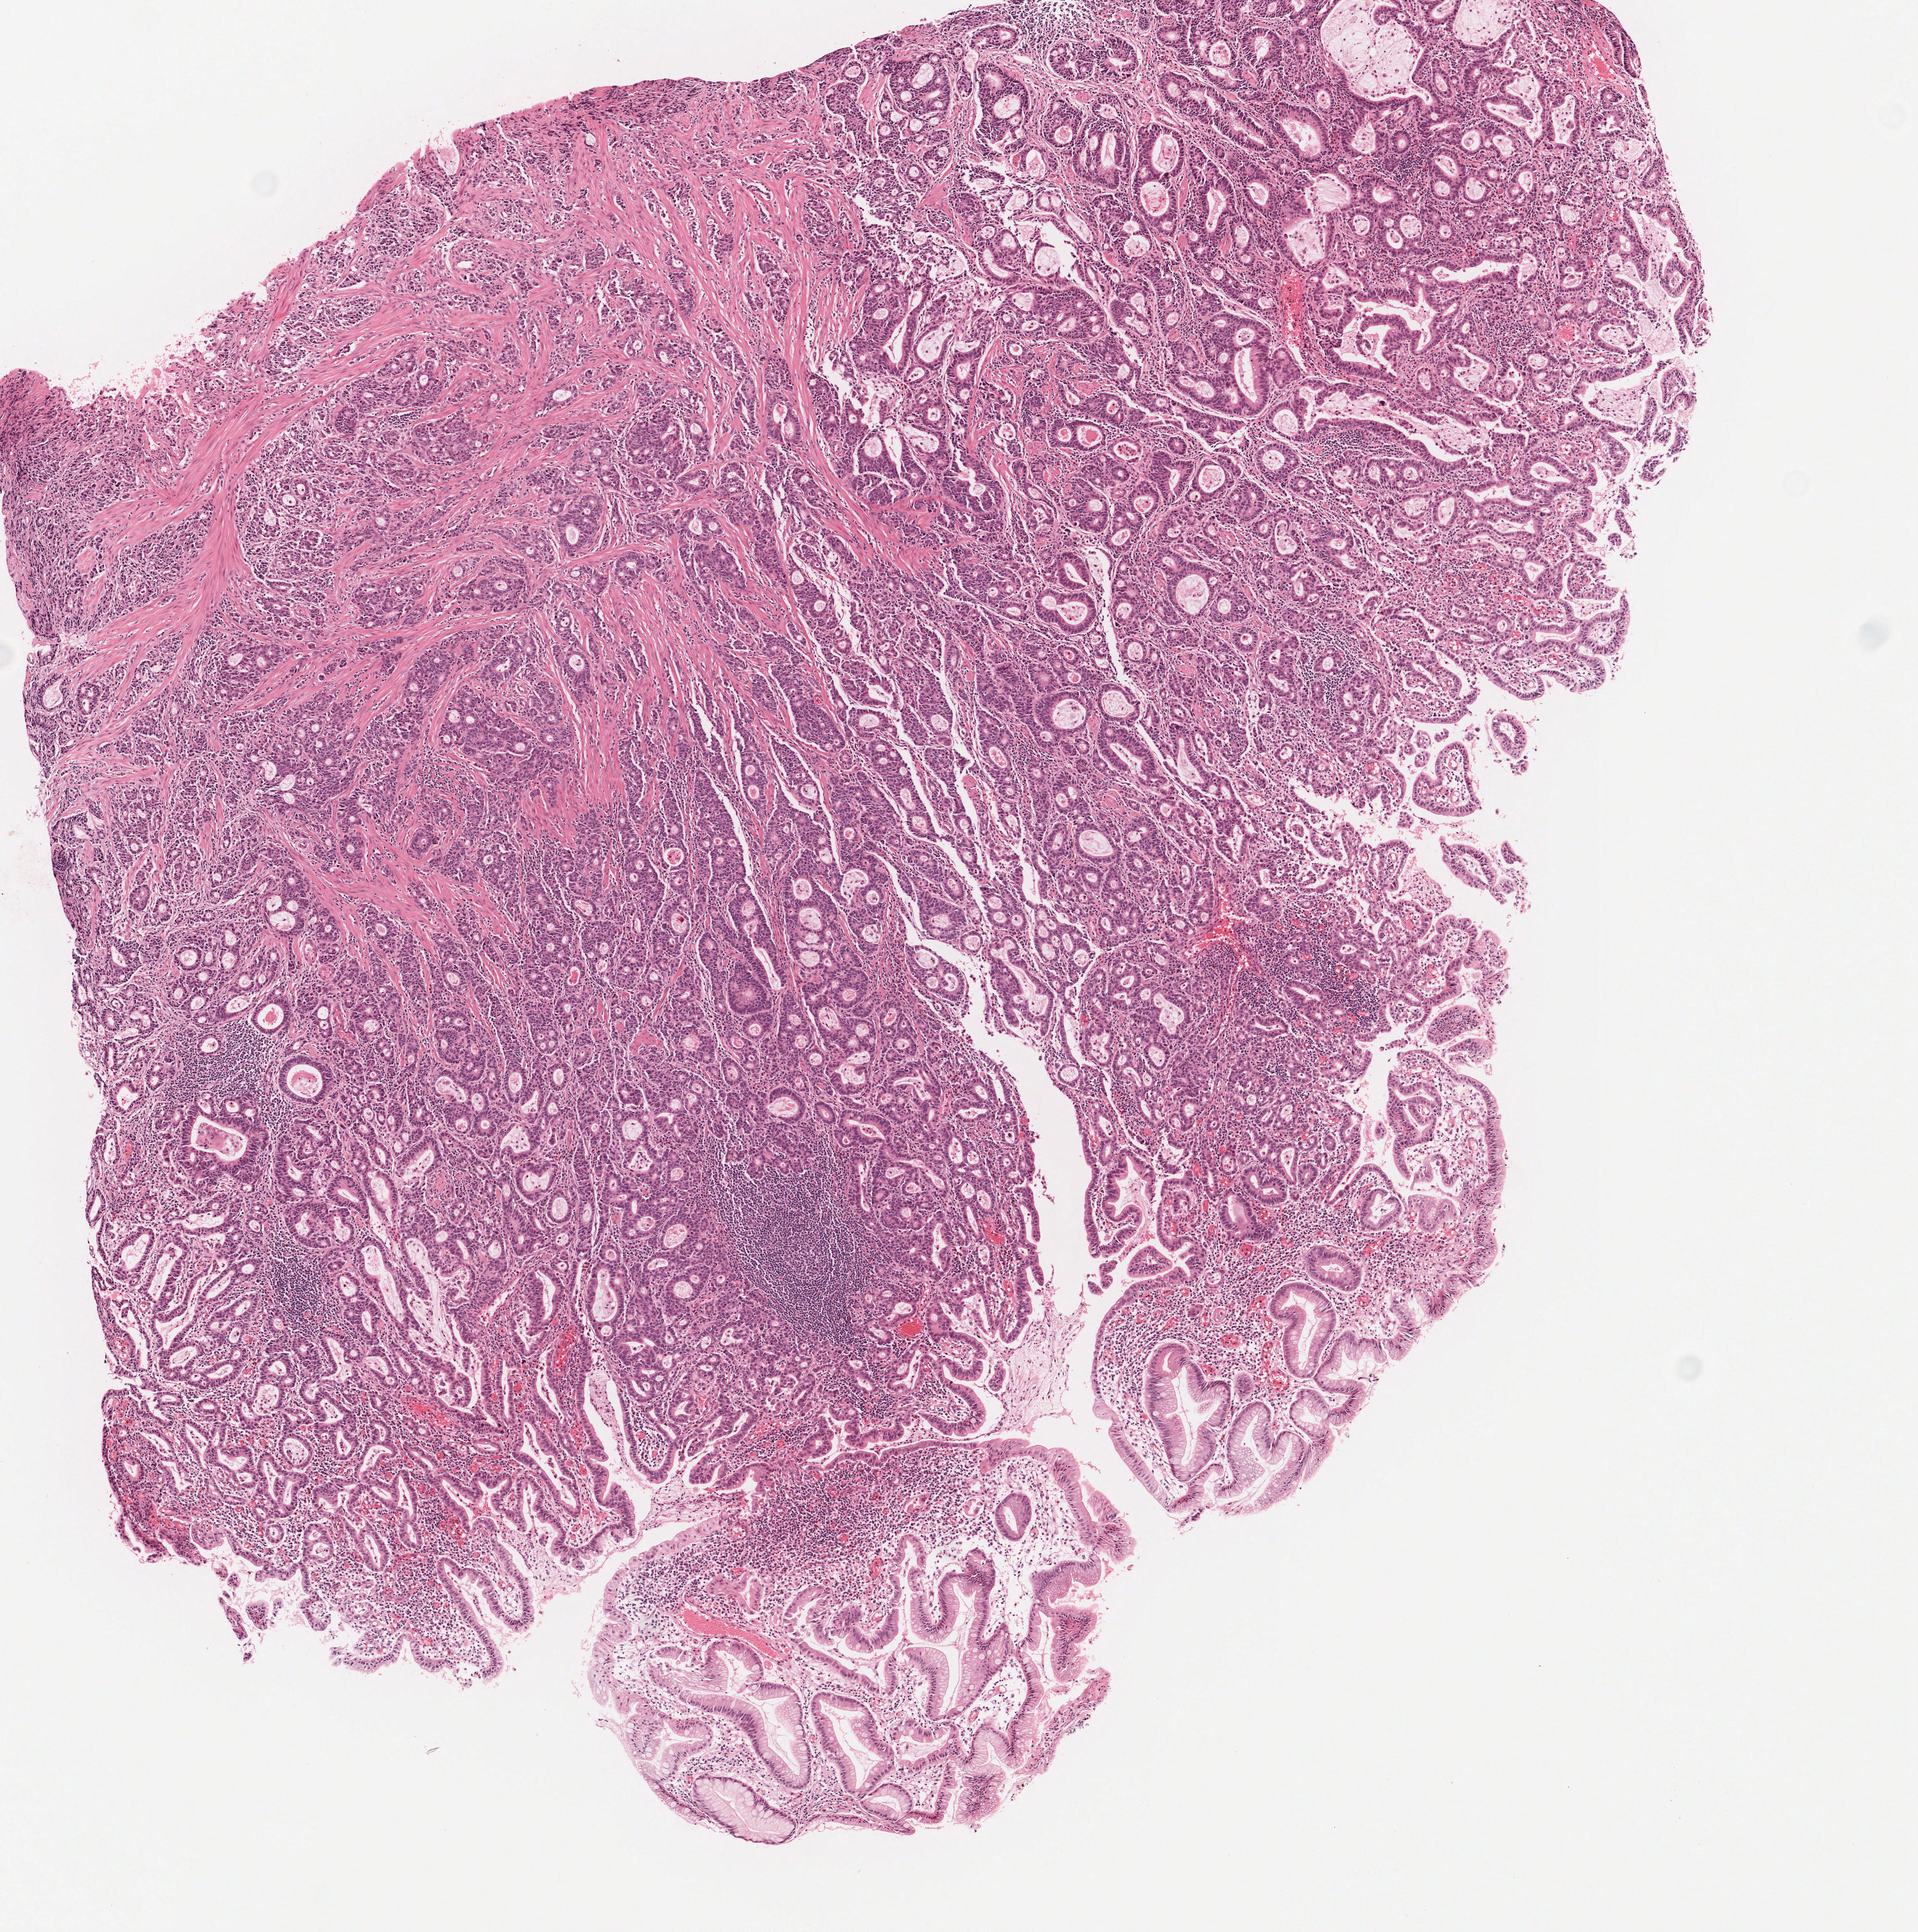
H&E whole-slide image — low-resolution overview of the scanned area, about 5.9 x 5.9 mm. FFPE section. Stomach, primary tumour sample. Patient: male, age at initial diagnosis 56 years. Histologic grade: G2 (moderately differentiated).
• pathologic diagnosis: Tubular adenocarcinoma
• lymph nodes positive (case pathology): 1 of 46 examined